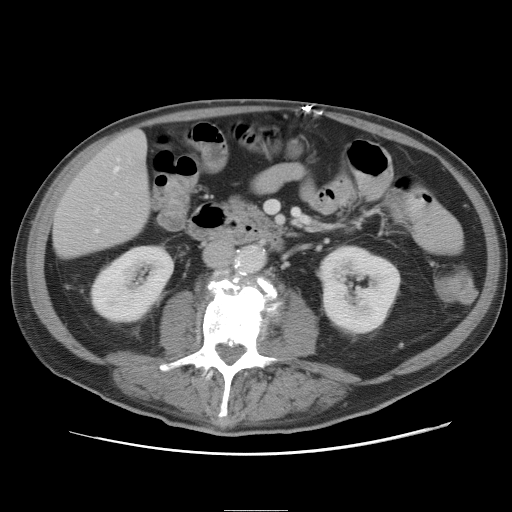
Contrast-enhanced abdominal CT, one axial slice; slice 14 of 89 in the series (ordered by position); 120 kVp; intravenous contrast given; soft-tissue window (W 400 / L 40 HU); 5 mm slice thickness; 512 × 512 image matrix. Male patient, age 69 years. Case-level facts recorded for this patient, not image findings: diagnosis: colorectal cancer liver metastases, imaged before liver resection; multiple liver metastases: no; largest metastasis: 8.5 cm; chemotherapy before resection: no.
Annotated regions visible in this slice (outlined manually by an expert reader):
- hepatic veins: box from (x=96, y=158) to (x=120, y=231) px
- liver: (x=55, y=131)–(x=151, y=258)
- planned liver remnant (the part of the liver to remain after resection): (x=54, y=131)–(x=151, y=258)